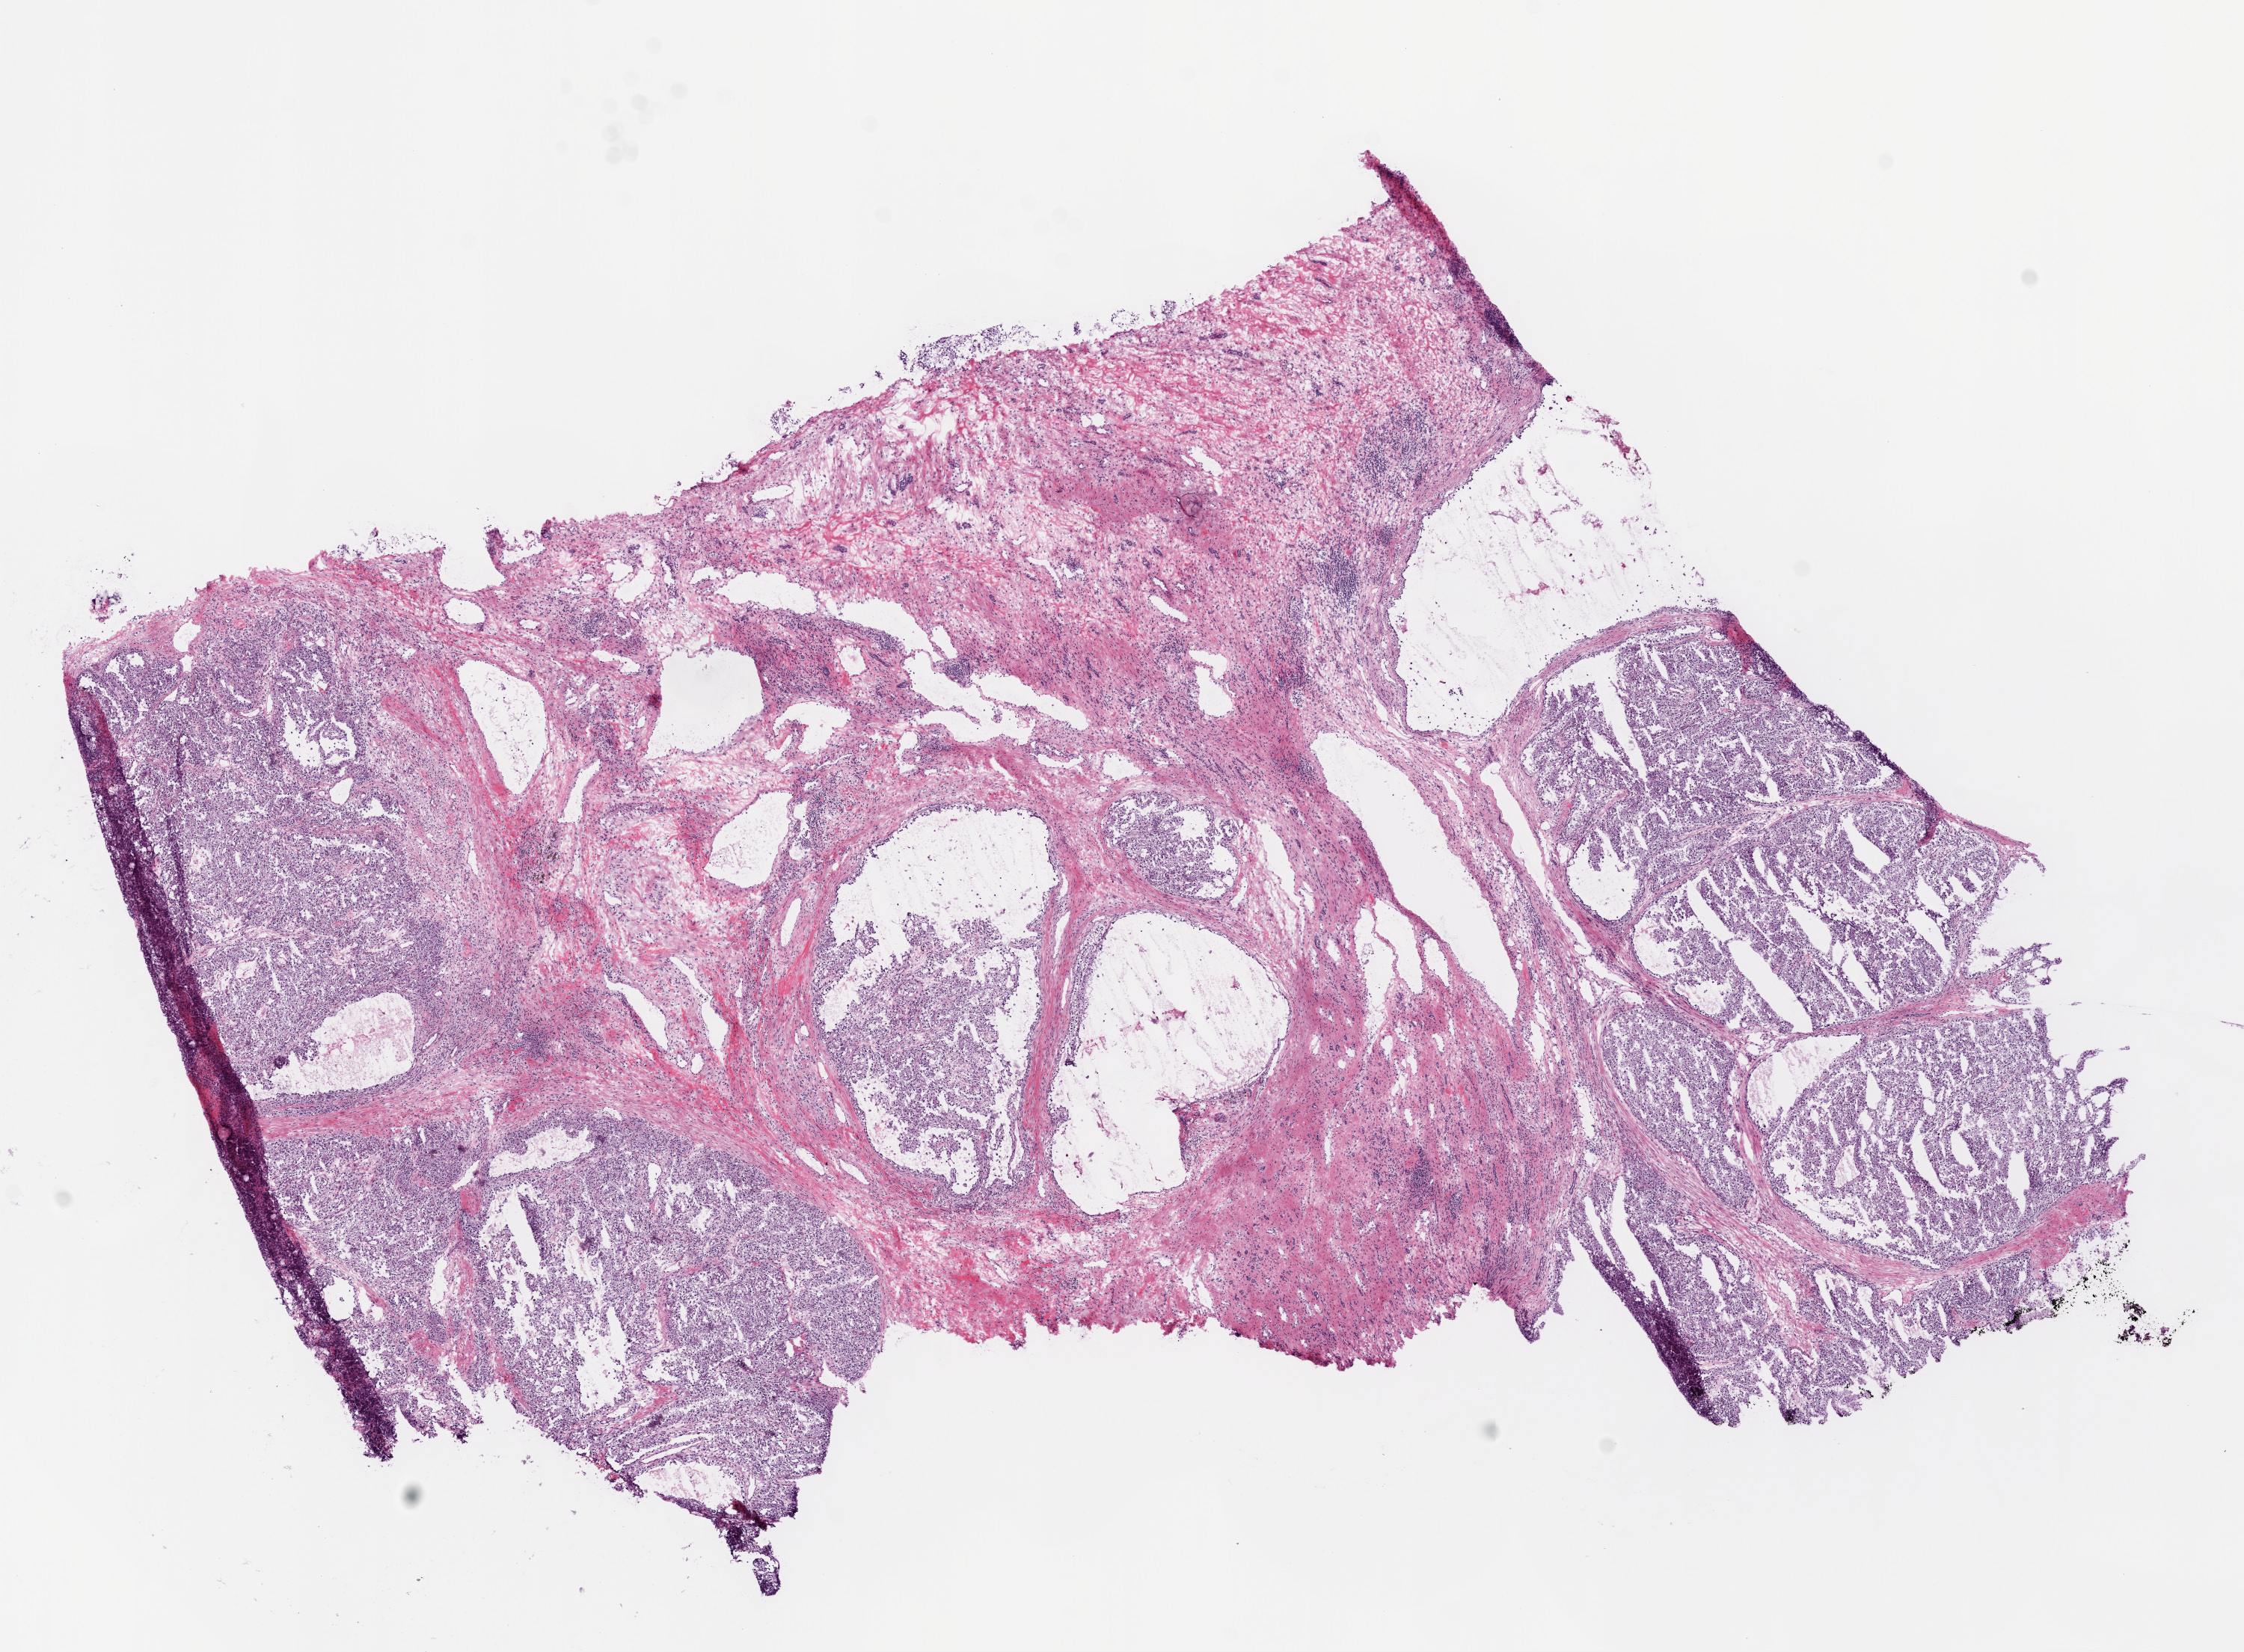
Whole-slide histology image, H&E, whole scanned area (about 12.0 x 8.9 mm, slide scanned at 20x) shown as a low-resolution overview, frozen section from the top of the tissue portion, kidney, primary tumour sample. Male patient; age at initial diagnosis 67 years. Histologic grade: G2 (moderately differentiated). Composition of this section per pathologist review: tumour cells 55%, tumour nuclei 80%, normal cells 30%, stromal cells 15%, necrosis 0%. Inflammatory infiltration, as recorded: lymphocyte infiltration 5%, monocyte infiltration 0%, neutrophil infiltration 0%.
- laterality: left
- pathologic diagnosis: Clear cell adenocarcinoma, NOS
- TNM: T2 N0 M0
- AJCC pathologic stage: II